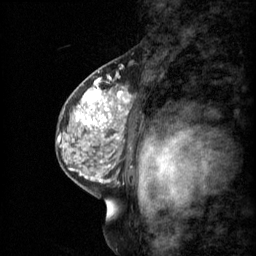
Breast MRI (dynamic contrast-enhanced), one sagittal slice; slice 41 of 60 in the series (ordered by position); 3 images stored at this slice position (order not interpretable as contrast timing); 1.5 T; TE 4.2 ms, TR 11 ms; 2 mm slice thickness; 256 × 256 image matrix. Patient: female, 48 years.
Structures marked on this image (semi-automatically segmented with operator editing):
- analysis volume of interest (the breast-tissue region the enhancement analysis was run in; not a lesion): box from (x=69, y=74) to (x=130, y=147) px
- tumour enhancement mask (voxels above the 70 % enhancement threshold inside the analysis volume of interest): (x=77, y=82)–(x=130, y=141)